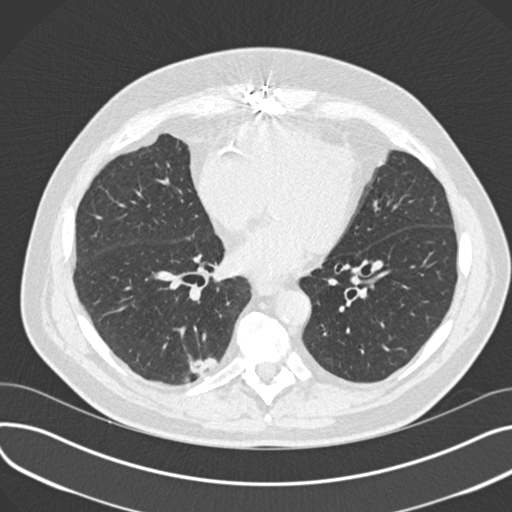
Low-dose screening chest CT, one axial slice; reconstruction kernel B30f; 120 kVp; lung window (W 1500 / L -600 HU); 512 × 512 image matrix.
Outlined on this slice (manually delineated by an expert):
- lesion 1 (tumor, lower lobe of right lung): bounding box (x1, y1, x2, y2) in pixels: (188, 354, 219, 378)